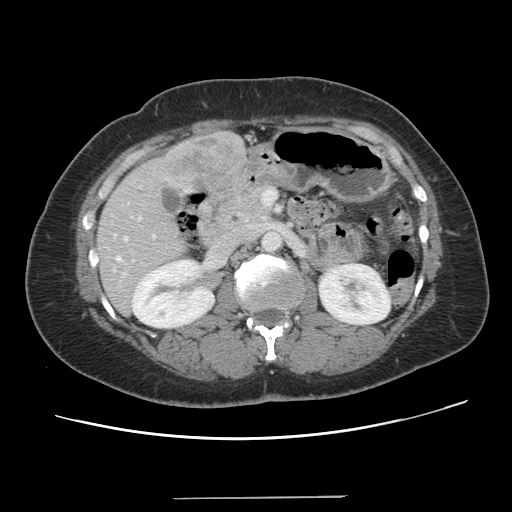
Contrast-enhanced abdominal CT, one axial slice. Slice 56 of 141 in the series (ordered by position). 120 kVp. Soft-tissue window (W 400 / L 40 HU). 2.5 mm slice thickness. 512 × 512 image matrix. Female patient, age 53 years. Case-level facts recorded for this patient, not image findings: diagnosis: colorectal cancer liver metastases, imaged before liver resection; multiple liver metastases: no; largest metastasis: 14.5 cm; disease in both lobes: yes.
Annotated regions visible in this slice (expert manual segmentation):
- hepatic veins: bounding box <116,237,126,260> (left, top, right, bottom; pixels)
- liver: <97,131,246,314>
- planned liver remnant (the part of the liver to remain after resection): <96,216,185,314>
- portal vein (with intrahepatic branches): <138,217,154,237>
- liver metastasis: <166,134,239,190>